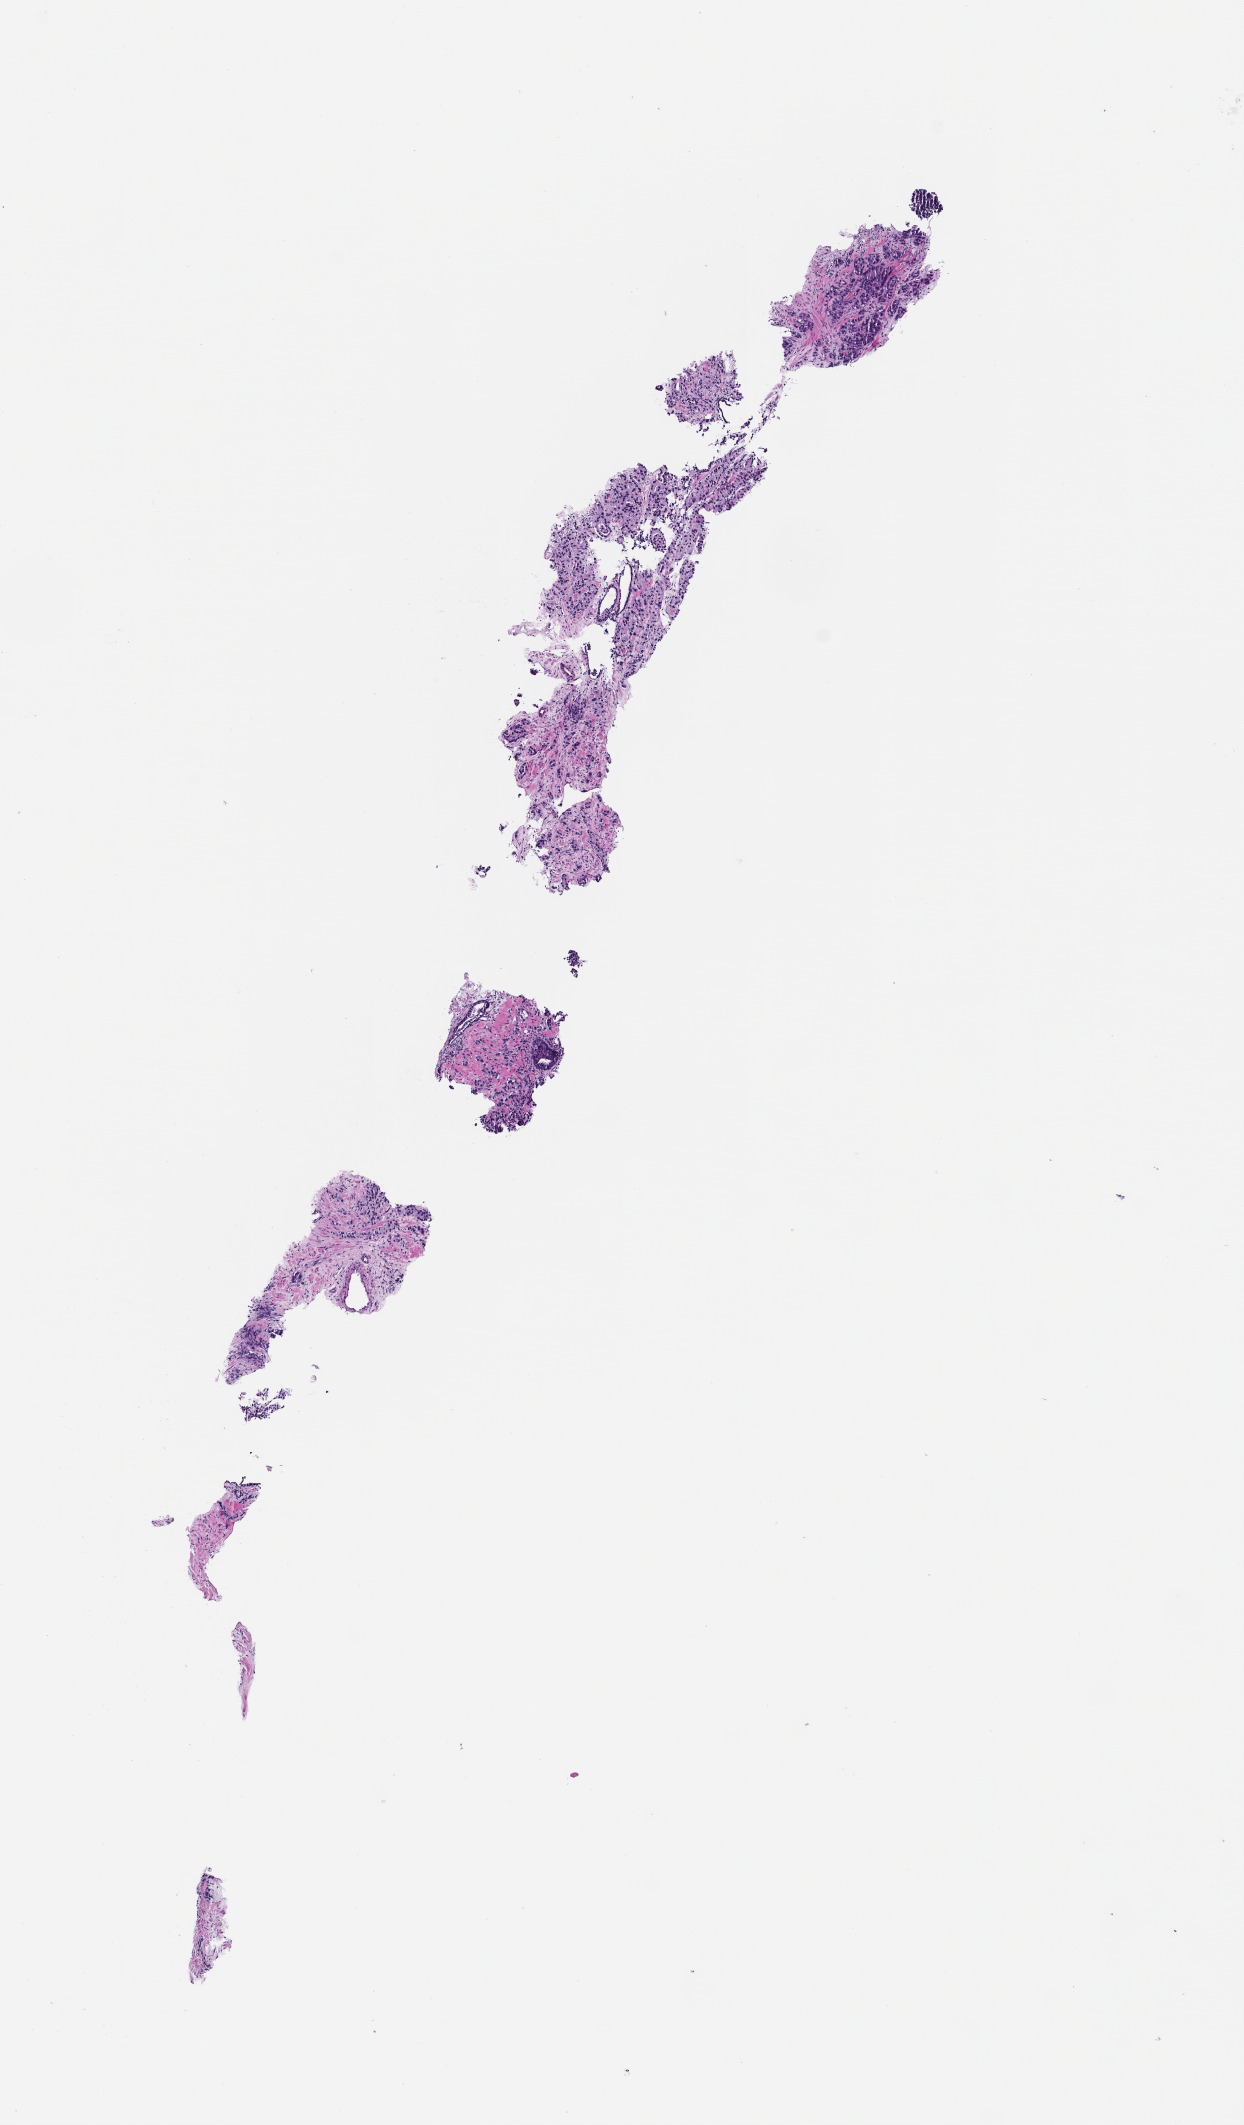
Digitized hematoxylin and eosin (H&E)-stained section, whole scanned area (about 5.0 x 8.6 mm) shown as a low-resolution overview; formalin-fixed paraffin-embedded section; site: prostate; specimen time point: archival tissue. Patient sex: male.
This section: primary tumour tissue. Diagnosis: Prostate Carcinoma.